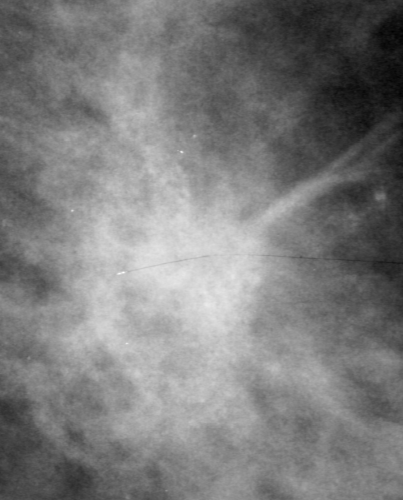
Crop from a digitized film mammogram around one marked abnormality, right breast, MLO view, BI-RADS breast density category 4 (scale 1–4).
Marked abnormality: calcifications, morphology pleomorphic, distribution clustered; BI-RADS assessment category 4; pathology result (as recorded, not read from the image): malignant.